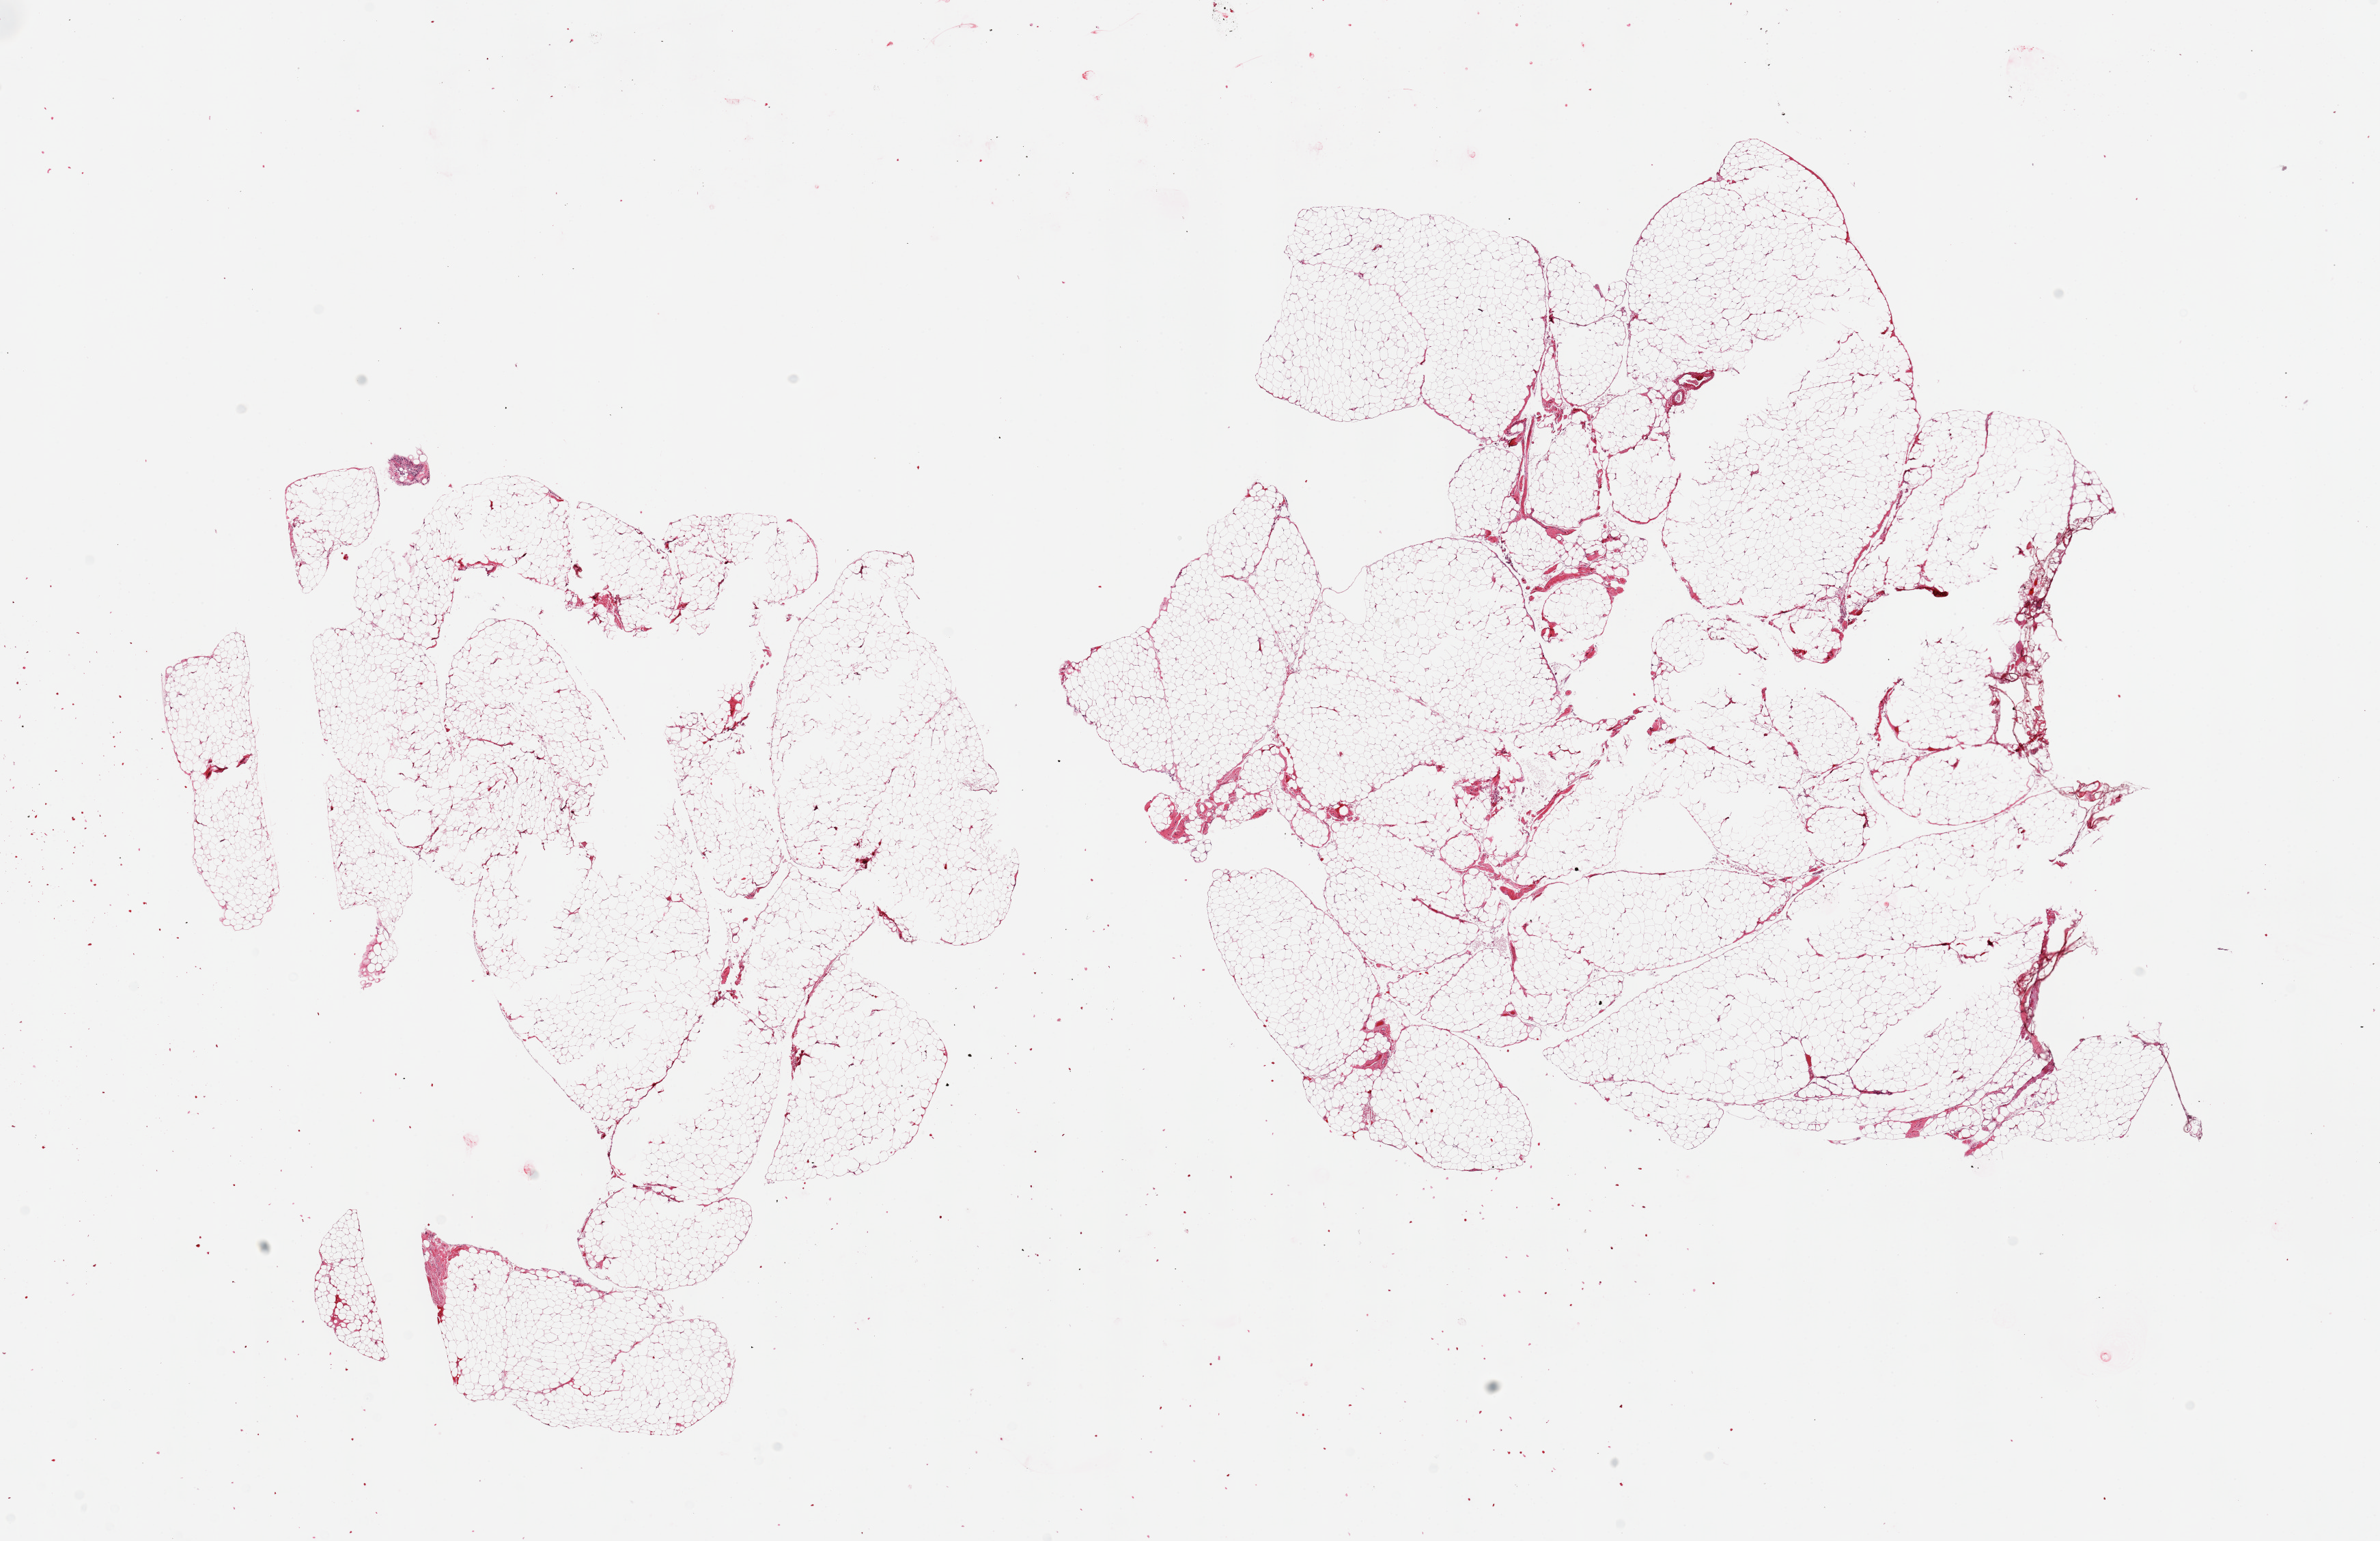
Digitized hematoxylin and eosin (H&E)-stained section — whole scanned area (about 27.6 x 17.9 mm, slide scanned at 20x) shown as a low-resolution overview. PAXgene-fixed, paraffin-embedded tissue. Sampled site (target tissue): omentum. Donor tissue sample. Donor sex: male.
- review note (as recorded): 2 pieces; one is oversized